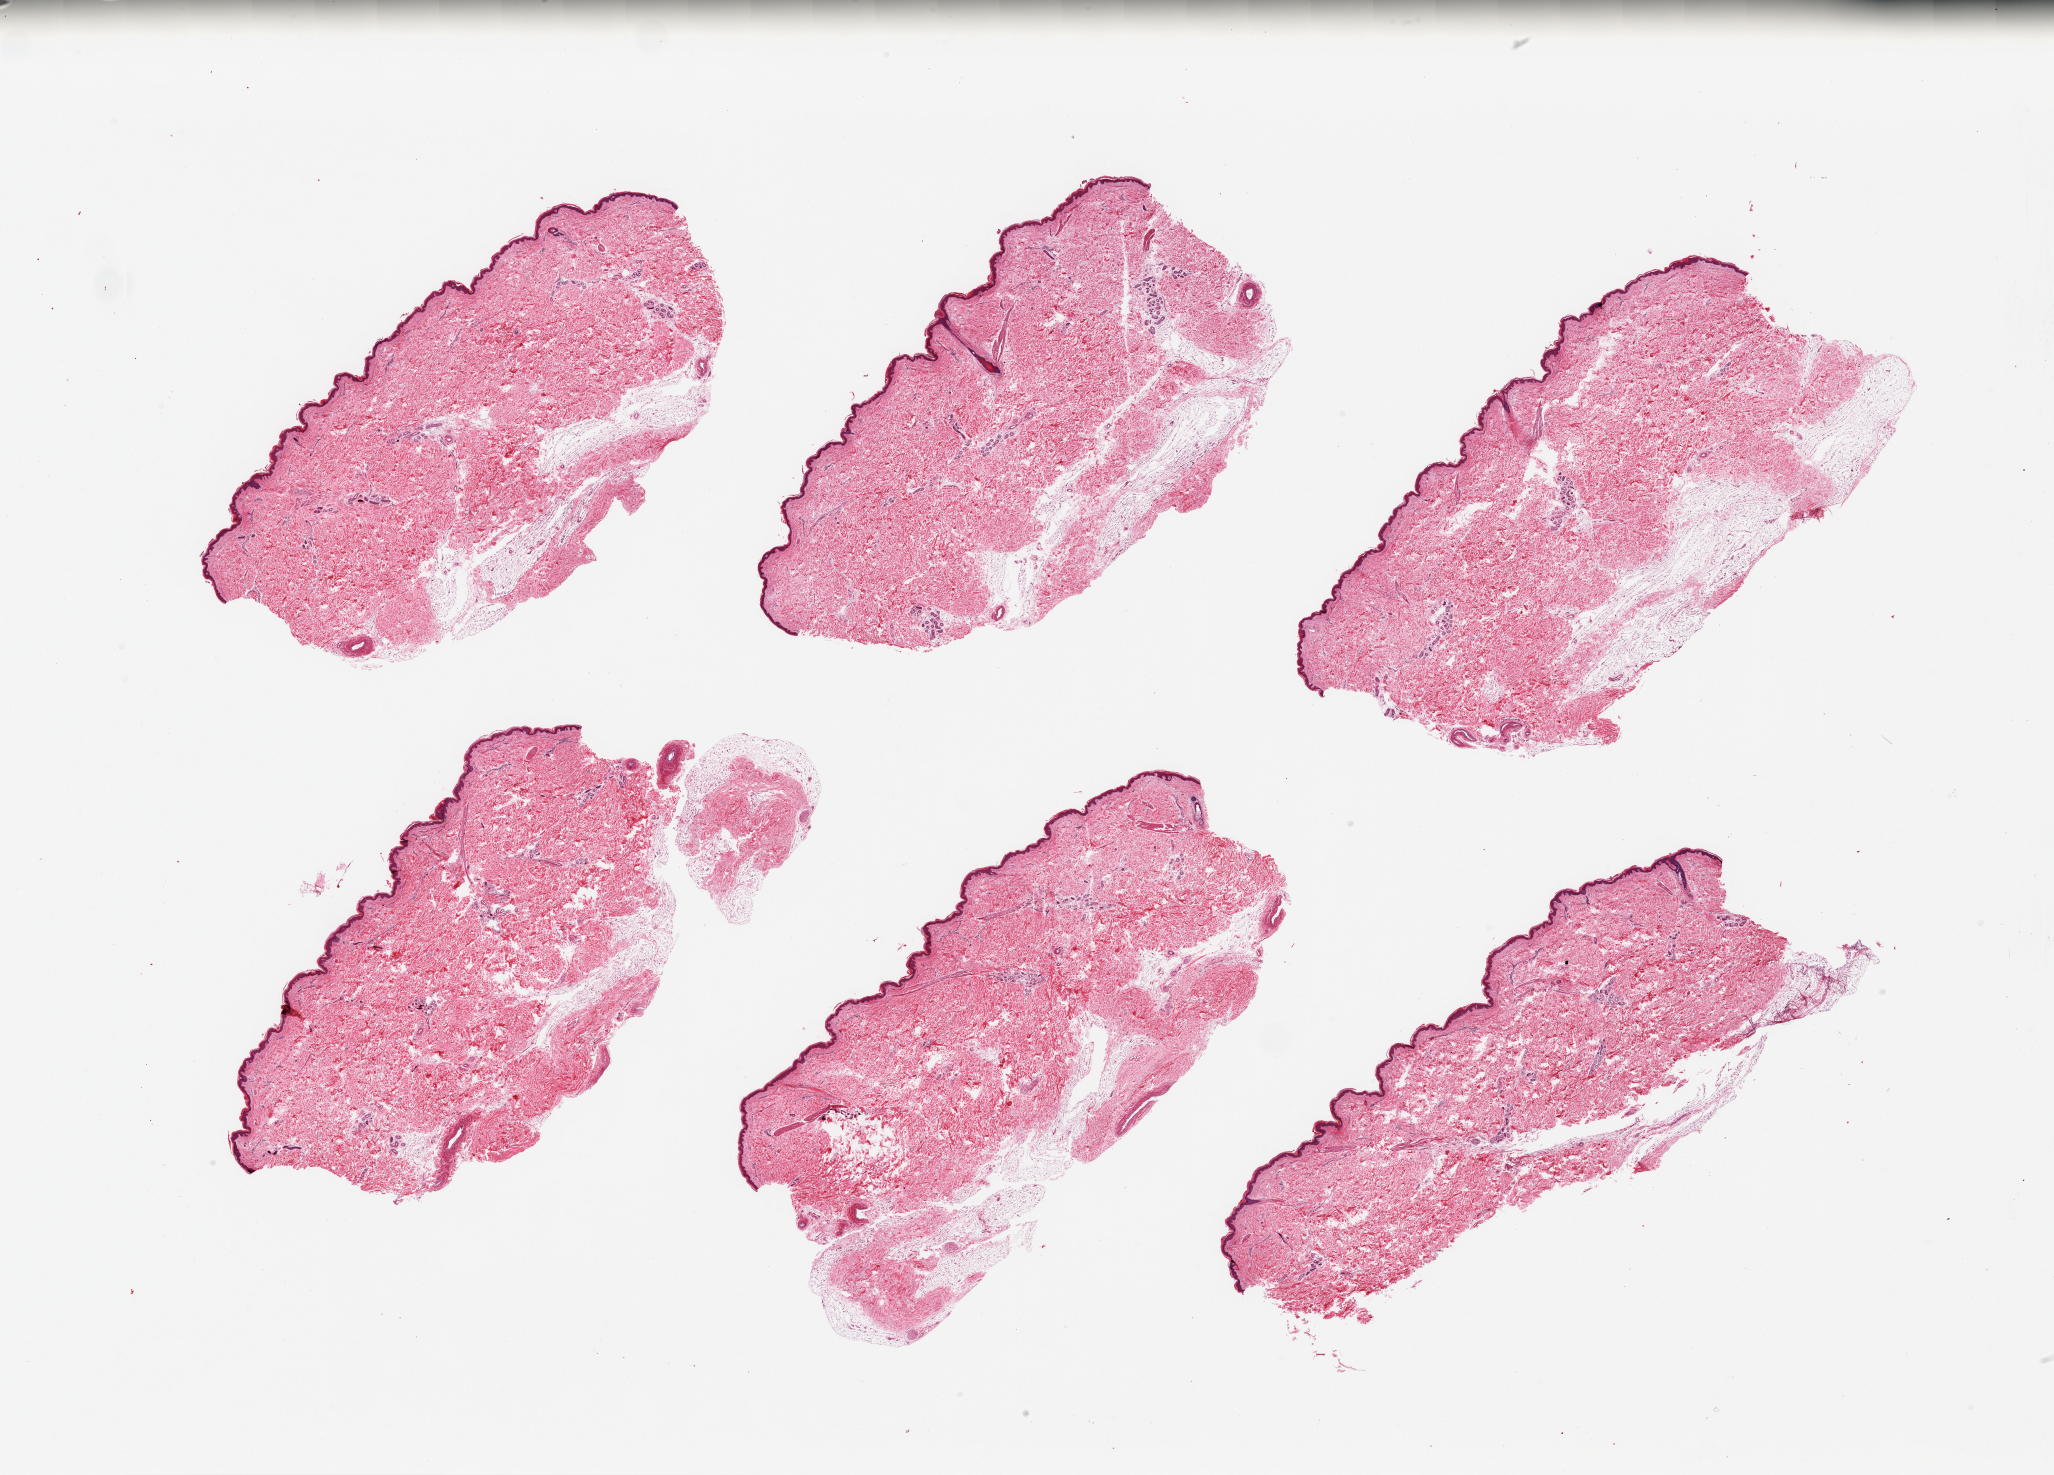
Whole-slide image, haematoxylin and eosin stain, shown as a low-resolution overview of the whole scanned area (about 32.5 x 23.3 mm, from a 20x scan). PAXgene-fixed, paraffin-embedded tissue. Target tissue: skin of lower leg. Donor tissue sample.
Reviewer comment on this tissue sample: 6 pieces; up to 20% moderately autolyzed internal/external fat; epidermis ~35 micron thick.